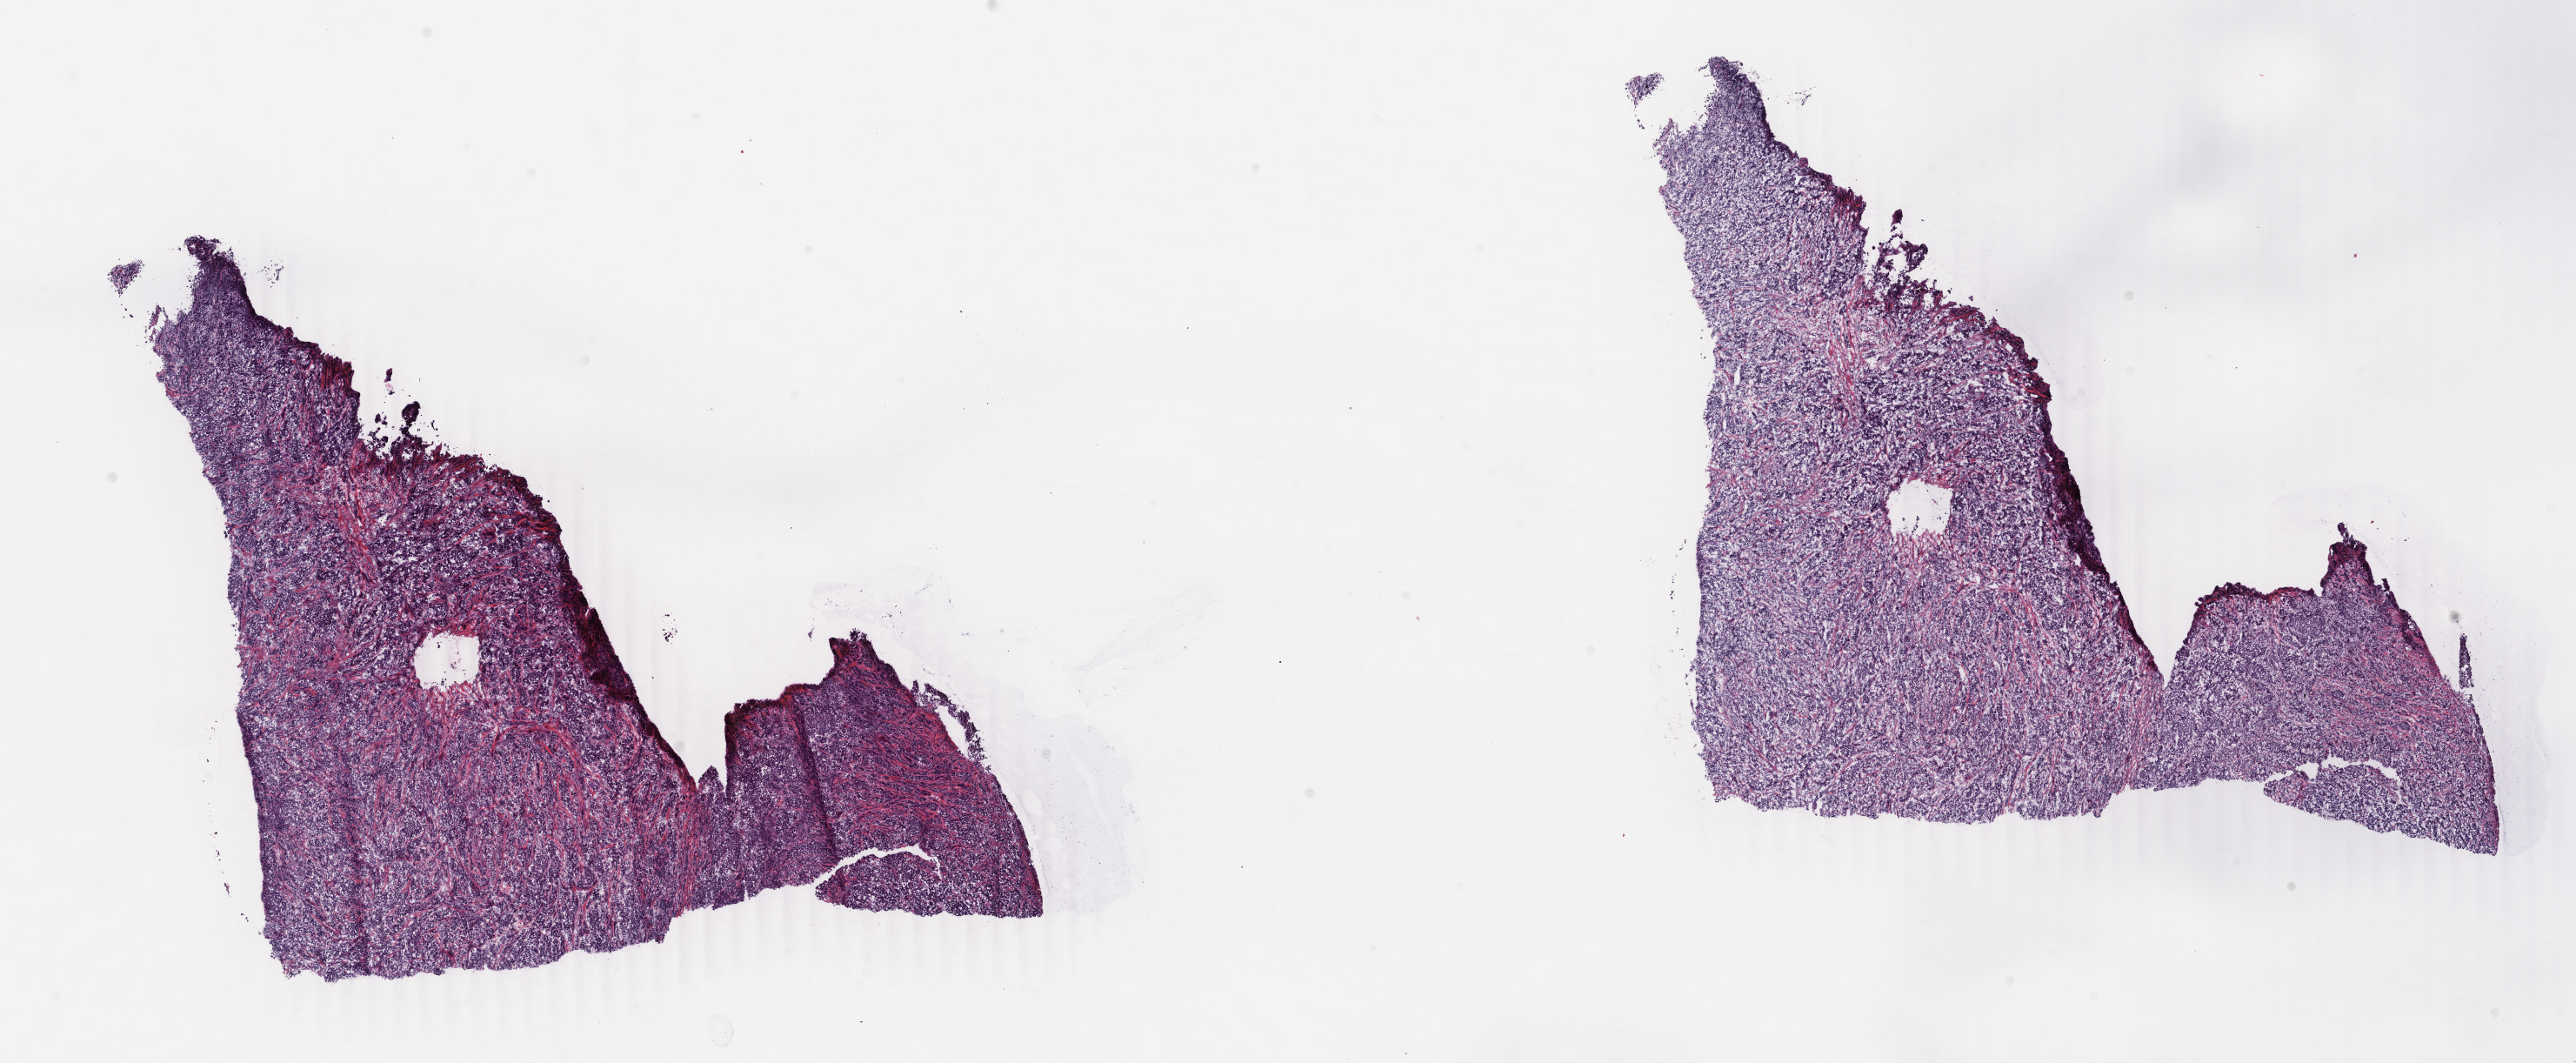
H&E-stained whole-slide image, a low-resolution overview of the entire scanned area, about 23.6 x 9.7 mm, frozen section from the bottom of the tissue portion, sample: primary tumour, breast. Female patient; age at initial diagnosis 50 years. Composition of this section per pathologist review: tumour cells 90%, tumour nuclei 90%, normal cells 0%, stromal cells 9%, necrosis 1%. Inflammatory infiltration, as recorded: lymphocyte infiltration 2%, monocyte infiltration 0%, neutrophil infiltration 0%.
Pathologic diagnosis: Infiltrating duct carcinoma, NOS. Laterality: right. AJCC pathologic stage: IIIA.